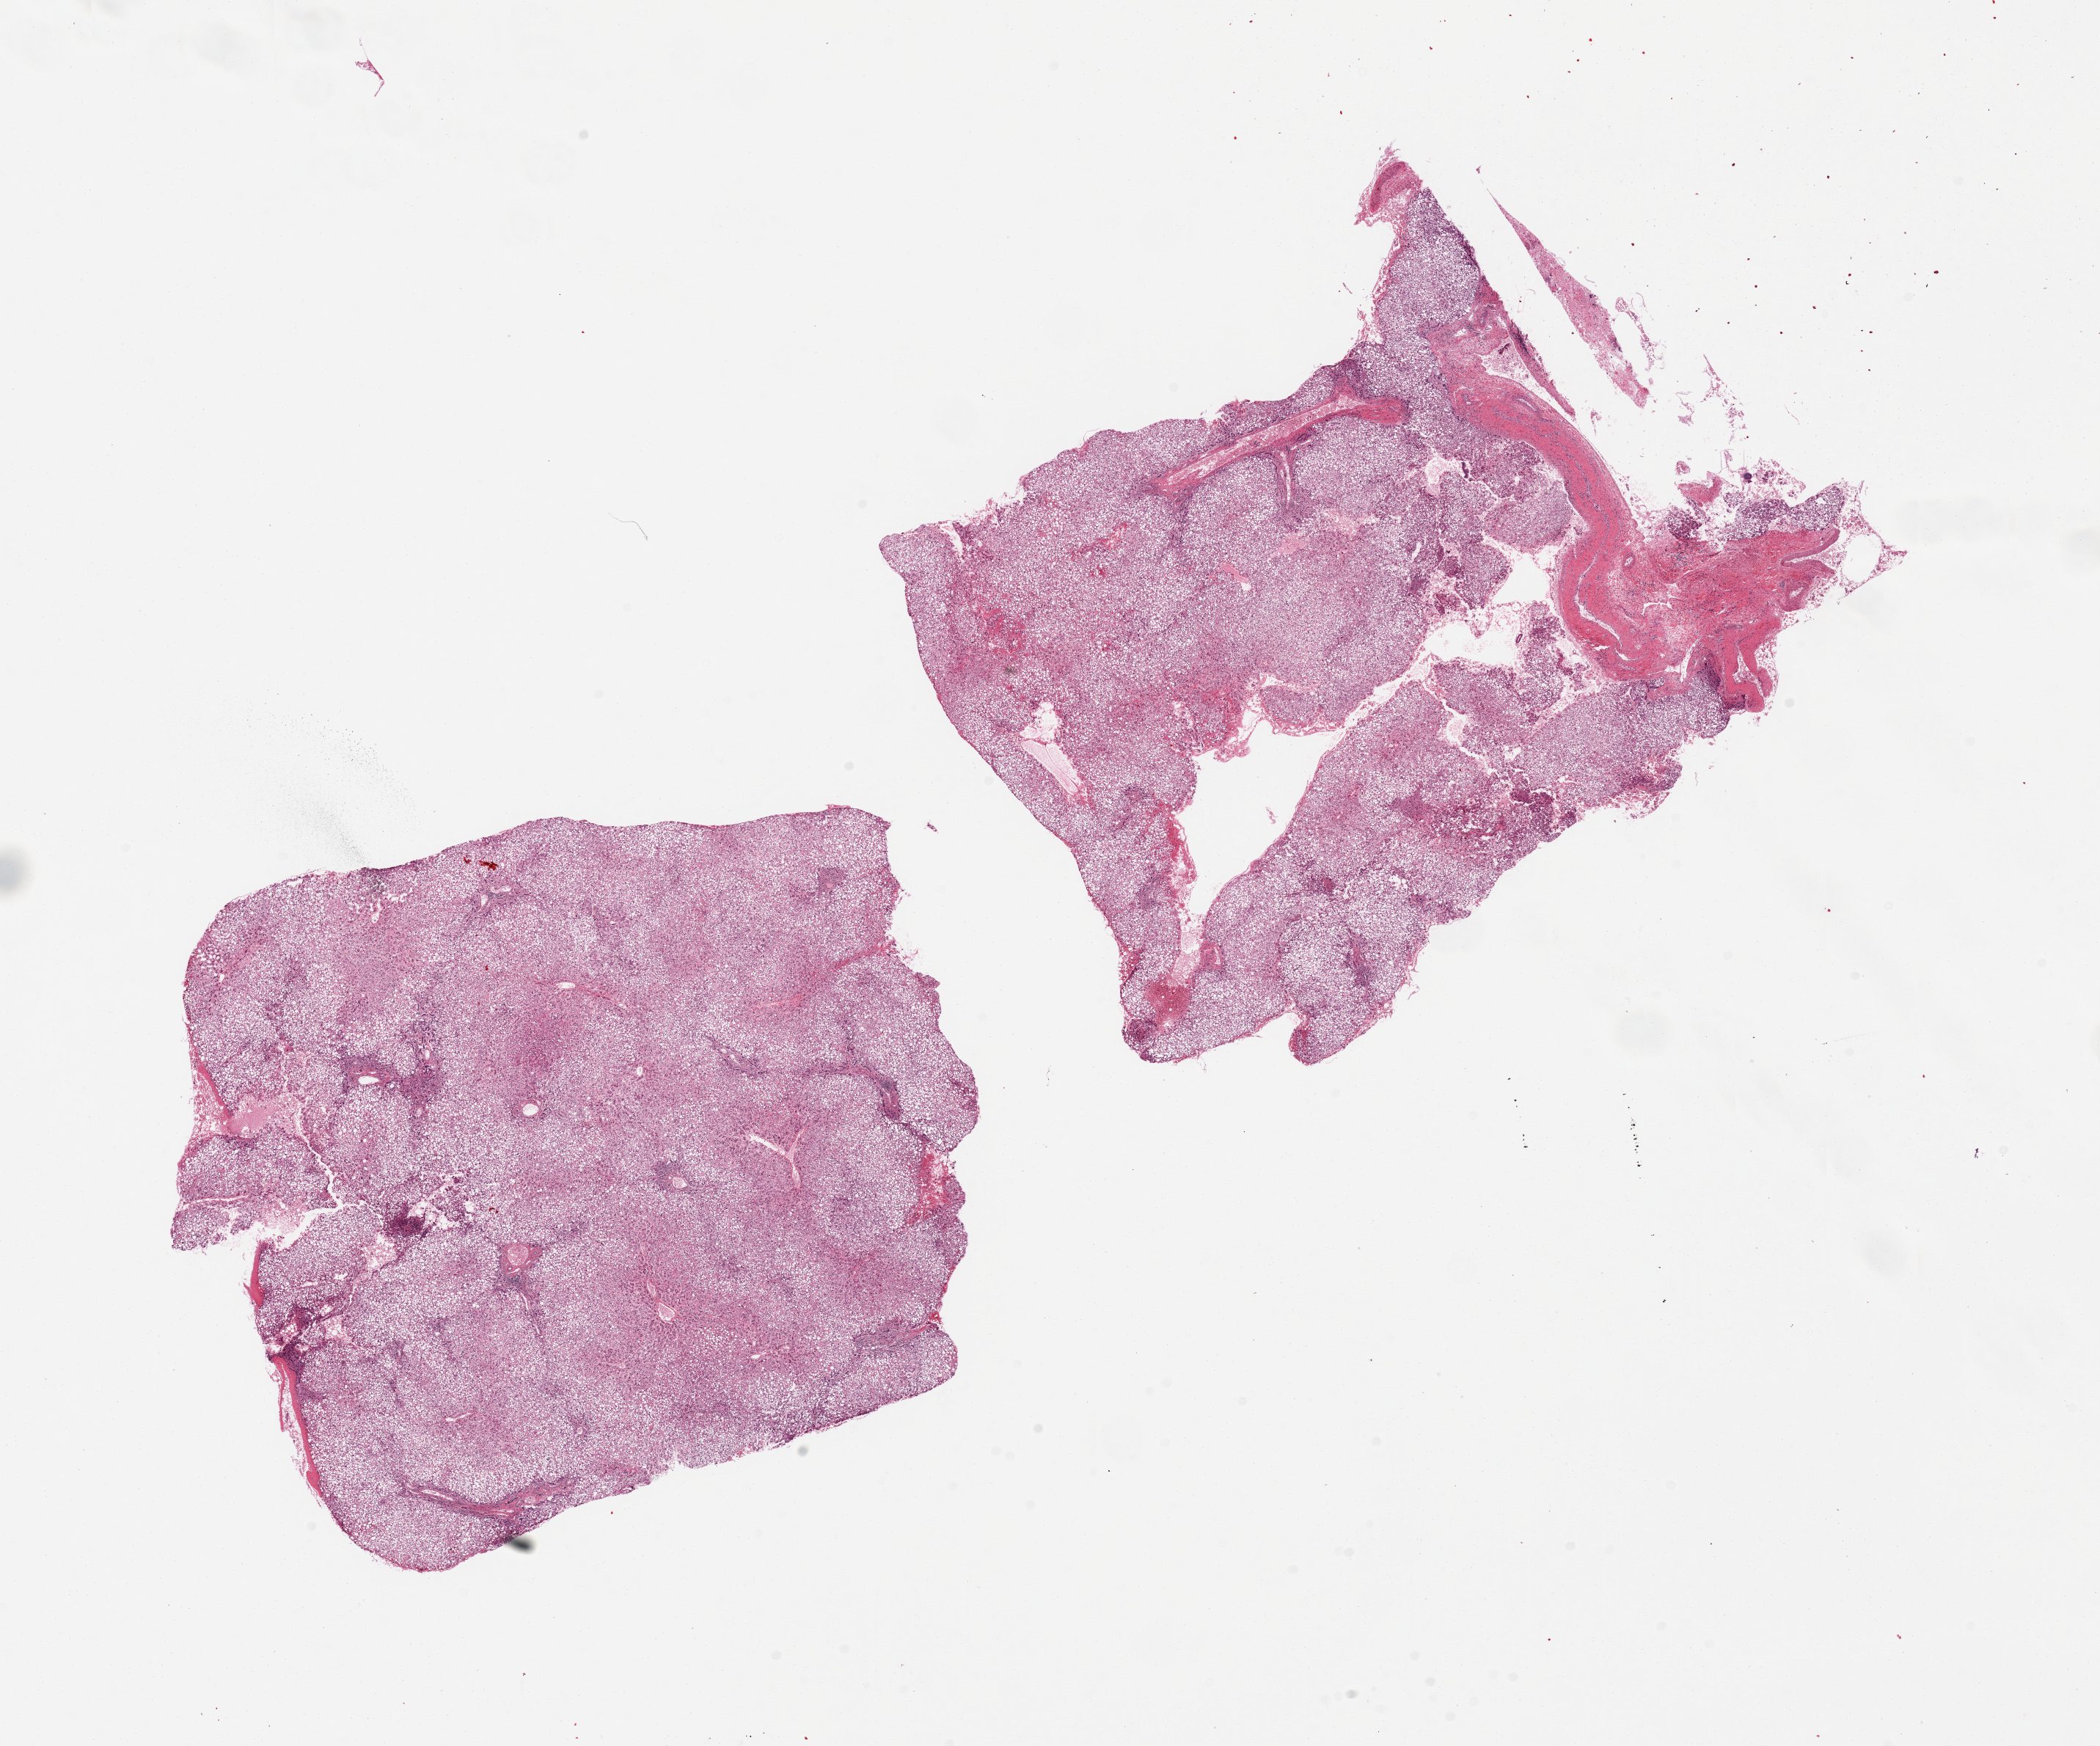
Whole-slide image, haematoxylin and eosin stain, brightfield, low-resolution overview of the scanned area, about 22.6 x 18.8 mm, PAXgene-fixed, paraffin-embedded tissue, sampled site (target tissue): liver, tissue donor sample.
* pathologist's review note for this sample: 2 pieces; severe macrovesicular steatosis